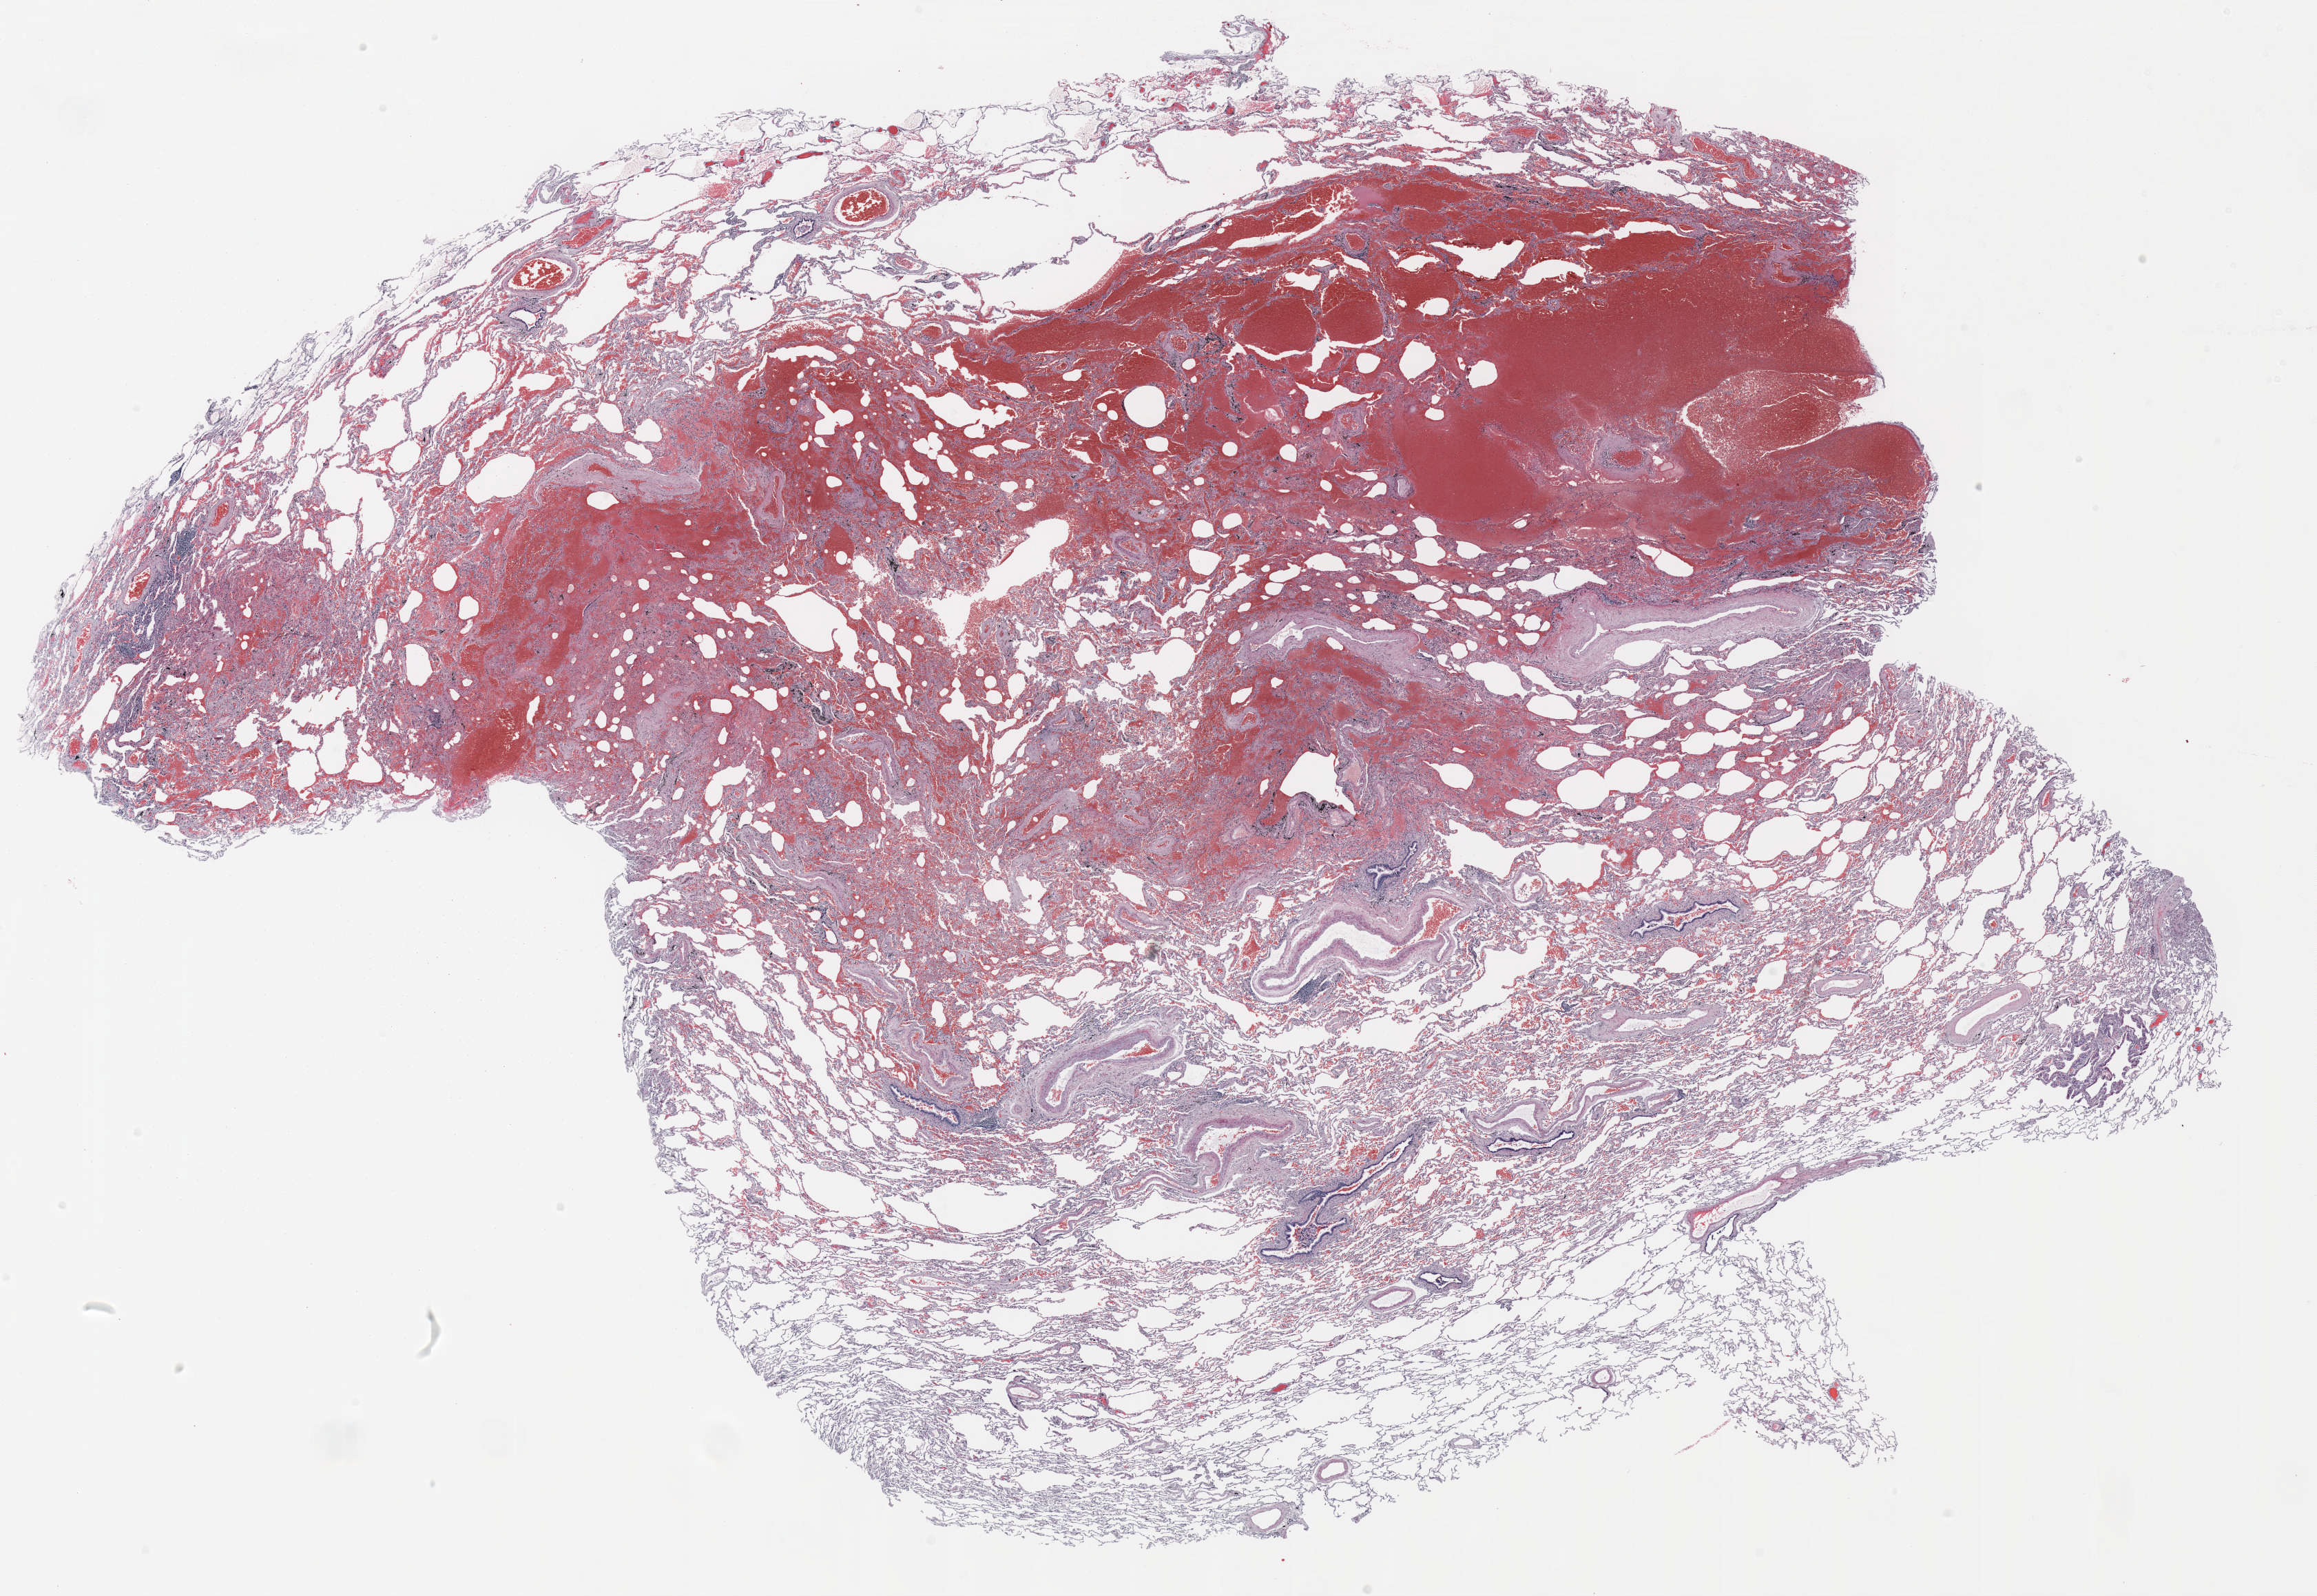
Whole-slide histology image, H&E, low-resolution overview of the scanned area, about 27.0 x 18.6 mm; formalin-fixed paraffin-embedded (FFPE) section; lung. Female, age 59 at enrolment. Grade: moderately differentiated (G2).
• participant's lung-cancer diagnosis: Adenocarcinoma, NOS
• stage (AJCC 6th edition): IIB
• primary tumour location (clinical record): right lower lobe
• tumour size (pathology): 22 mm